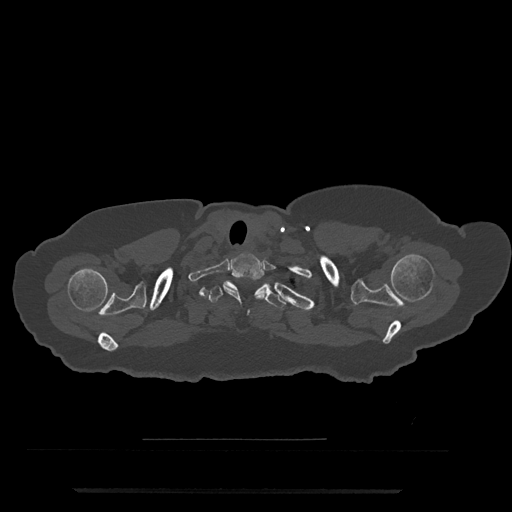
CT including the spine, one axial slice; position 695 of 797 along the scan axis; reconstruction kernel Br40s/3; bone window (W 1800 / L 400 HU); 0.5 mm slice thickness; 512 × 512 image matrix, field of view 440 × 440 mm. Patient: female, 51 years. Case-level facts recorded for this patient, not image findings: primary cancer: neuro; vertebrae with lytic lesions (as recorded): T8.
Outlined on this slice (semi-automatically segmented with operator editing):
- T1 vertebra: bounding box (x1, y1, x2, y2) in pixels: (223, 254, 266, 314)
- T2 vertebra: (207, 280, 286, 310)